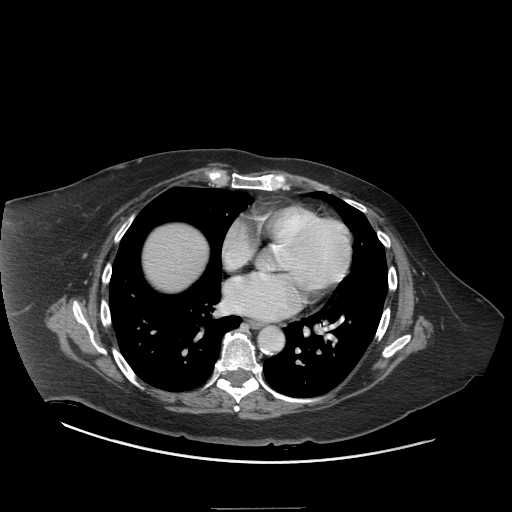
Contrast-enhanced abdominal CT (liver protocol), one axial slice; position 75 of 81 along the scan axis; soft-tissue window (W 400 / L 40 HU); 2.5 mm slice thickness; 512 × 512 image matrix, field of view 440 × 440 mm. Case-level facts recorded for this patient, not image findings: diagnosis: hepatocellular carcinoma (patient treated with transarterial chemoembolisation; whether this scan precedes or follows treatment is not stated here); TNM stage (as recorded): Stage-II; Child-Pugh class: A; tumour differentiation: moderately differentiated; tumour nodularity: multinodular.
Annotated regions visible in this slice (semi-automatic segmentation, software-assisted and operator-edited):
- liver parenchyma outside the tumour (the mass and vessels are separate outlines, so this box may not span the whole liver): bounding box <144,224,208,290> (left, top, right, bottom; pixels)